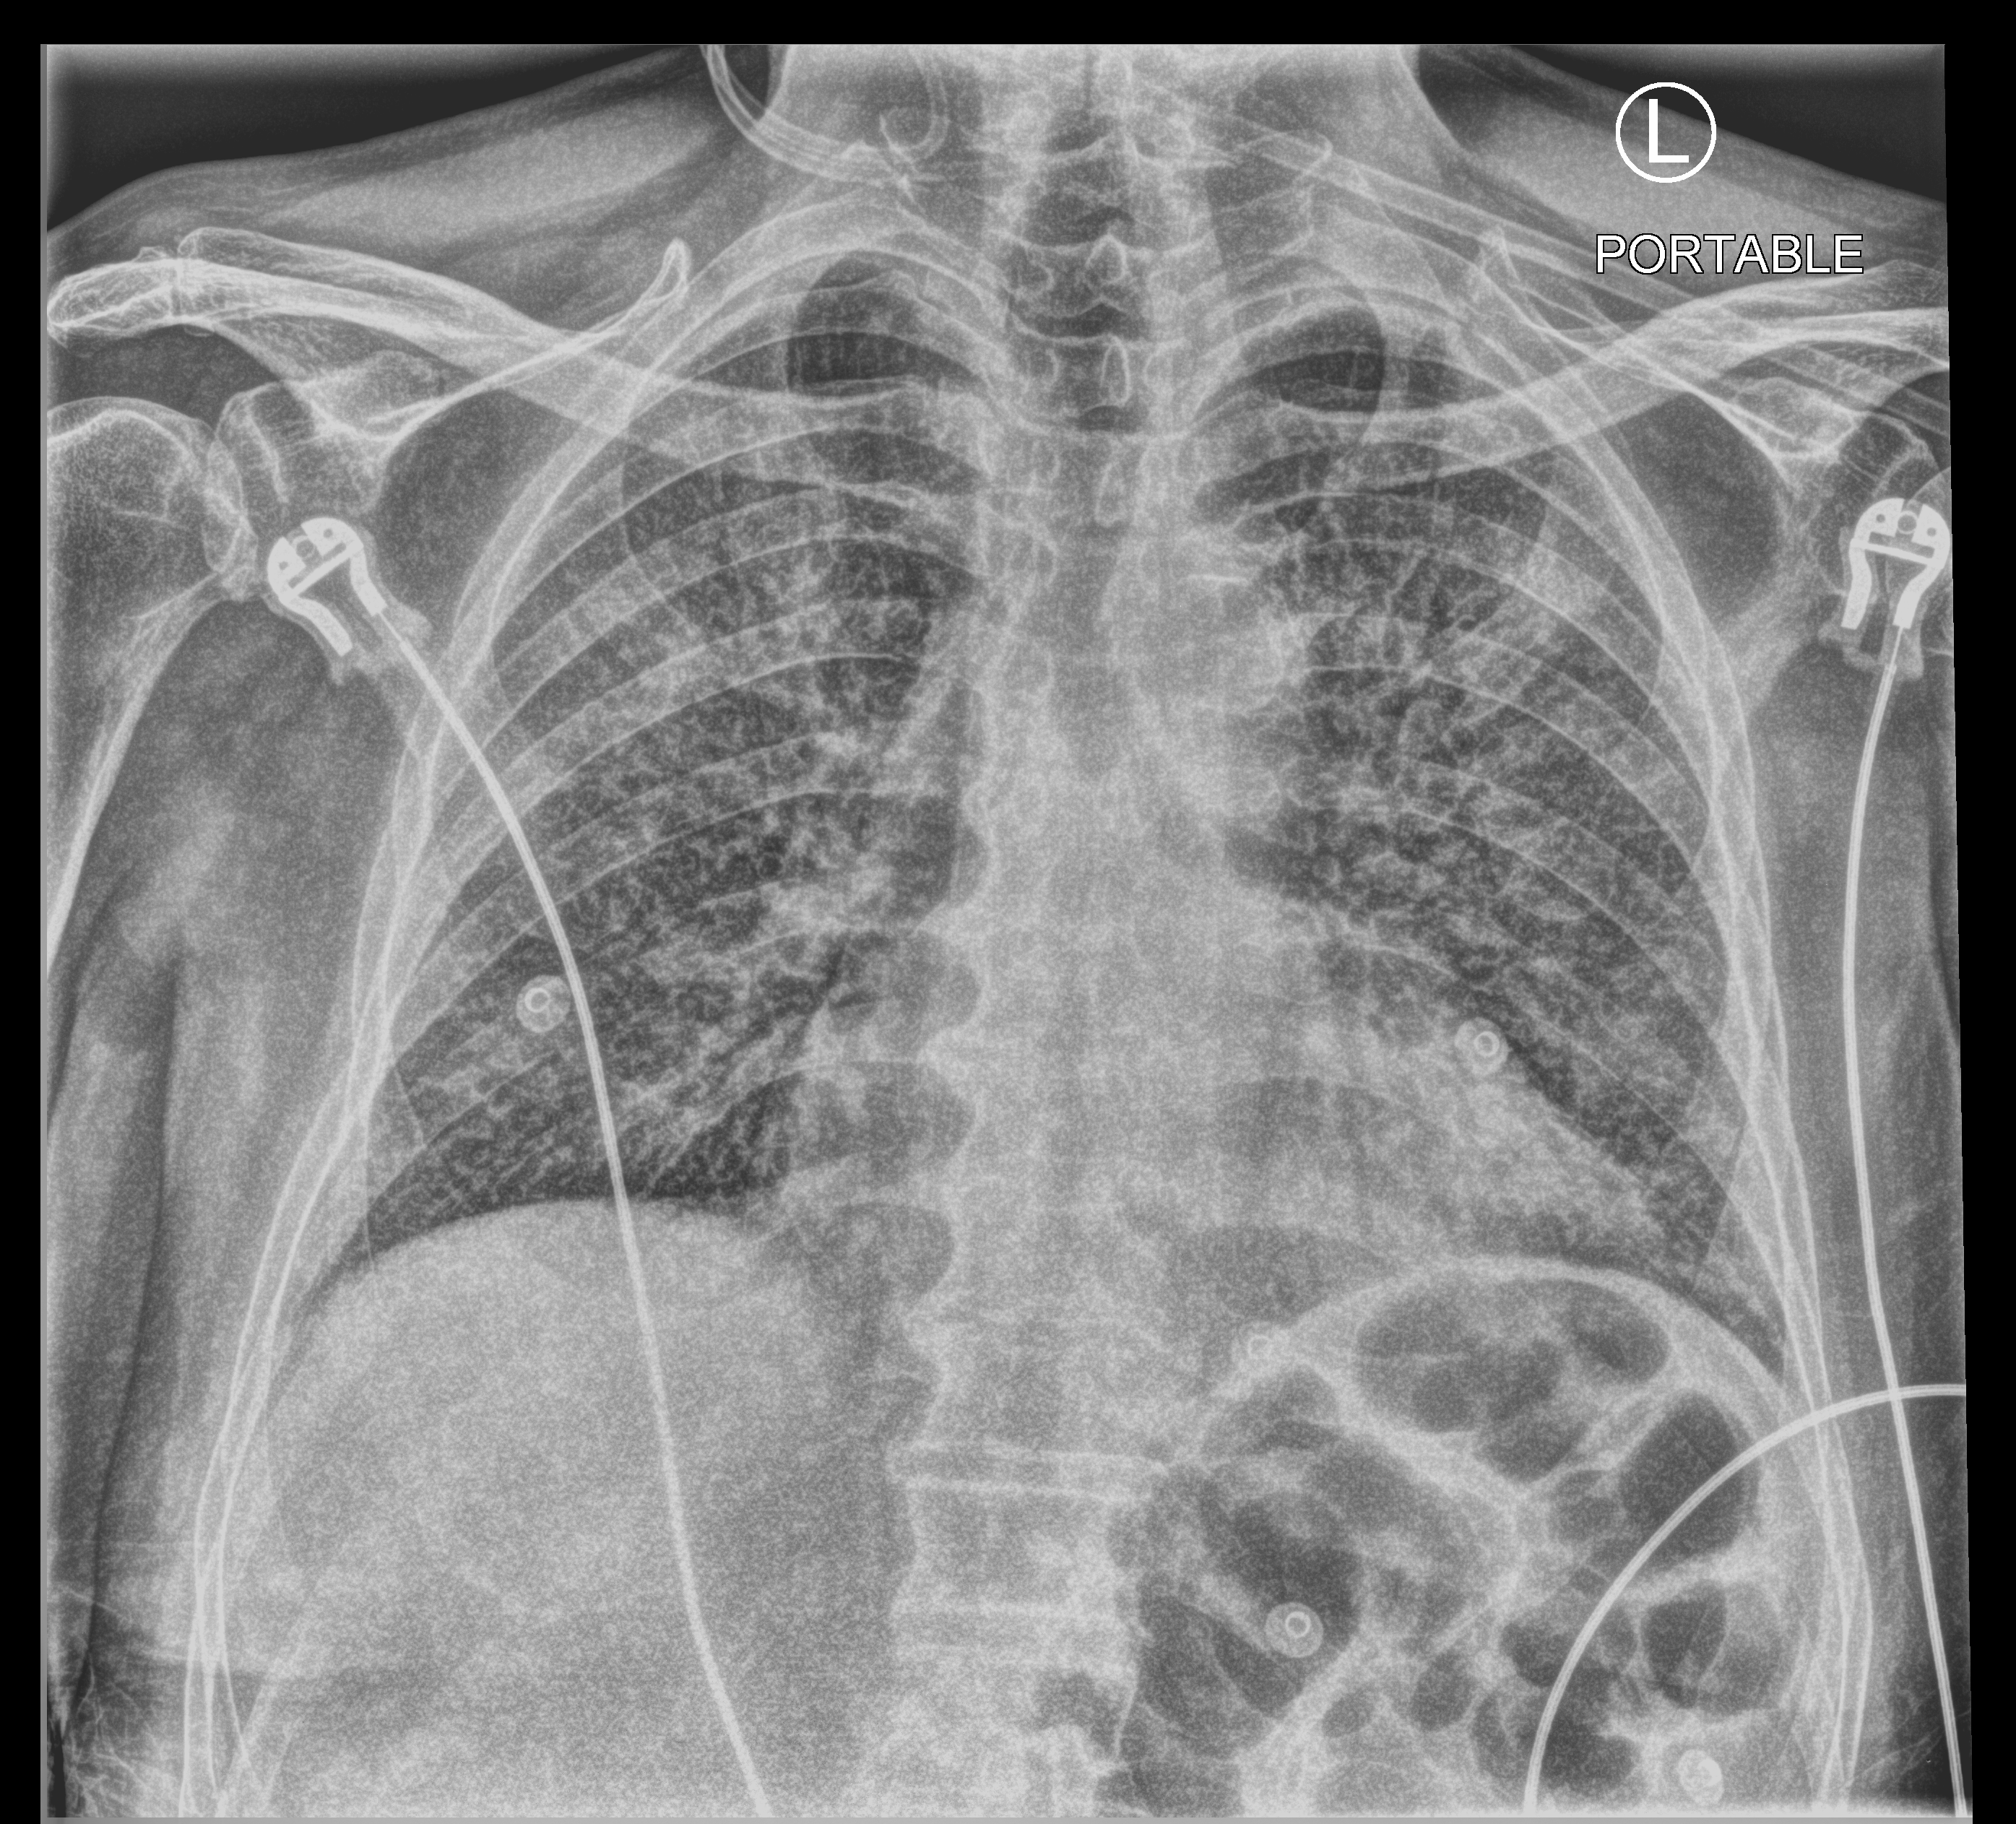
Chest X-ray (portable); anteroposterior (AP) projection. Male patient hospitalised with COVID-19, age 75–90 years.
From the hospital-stay record, not from the radiograph (when in the stay this image was taken is not recorded):
- COPD (admission record): no